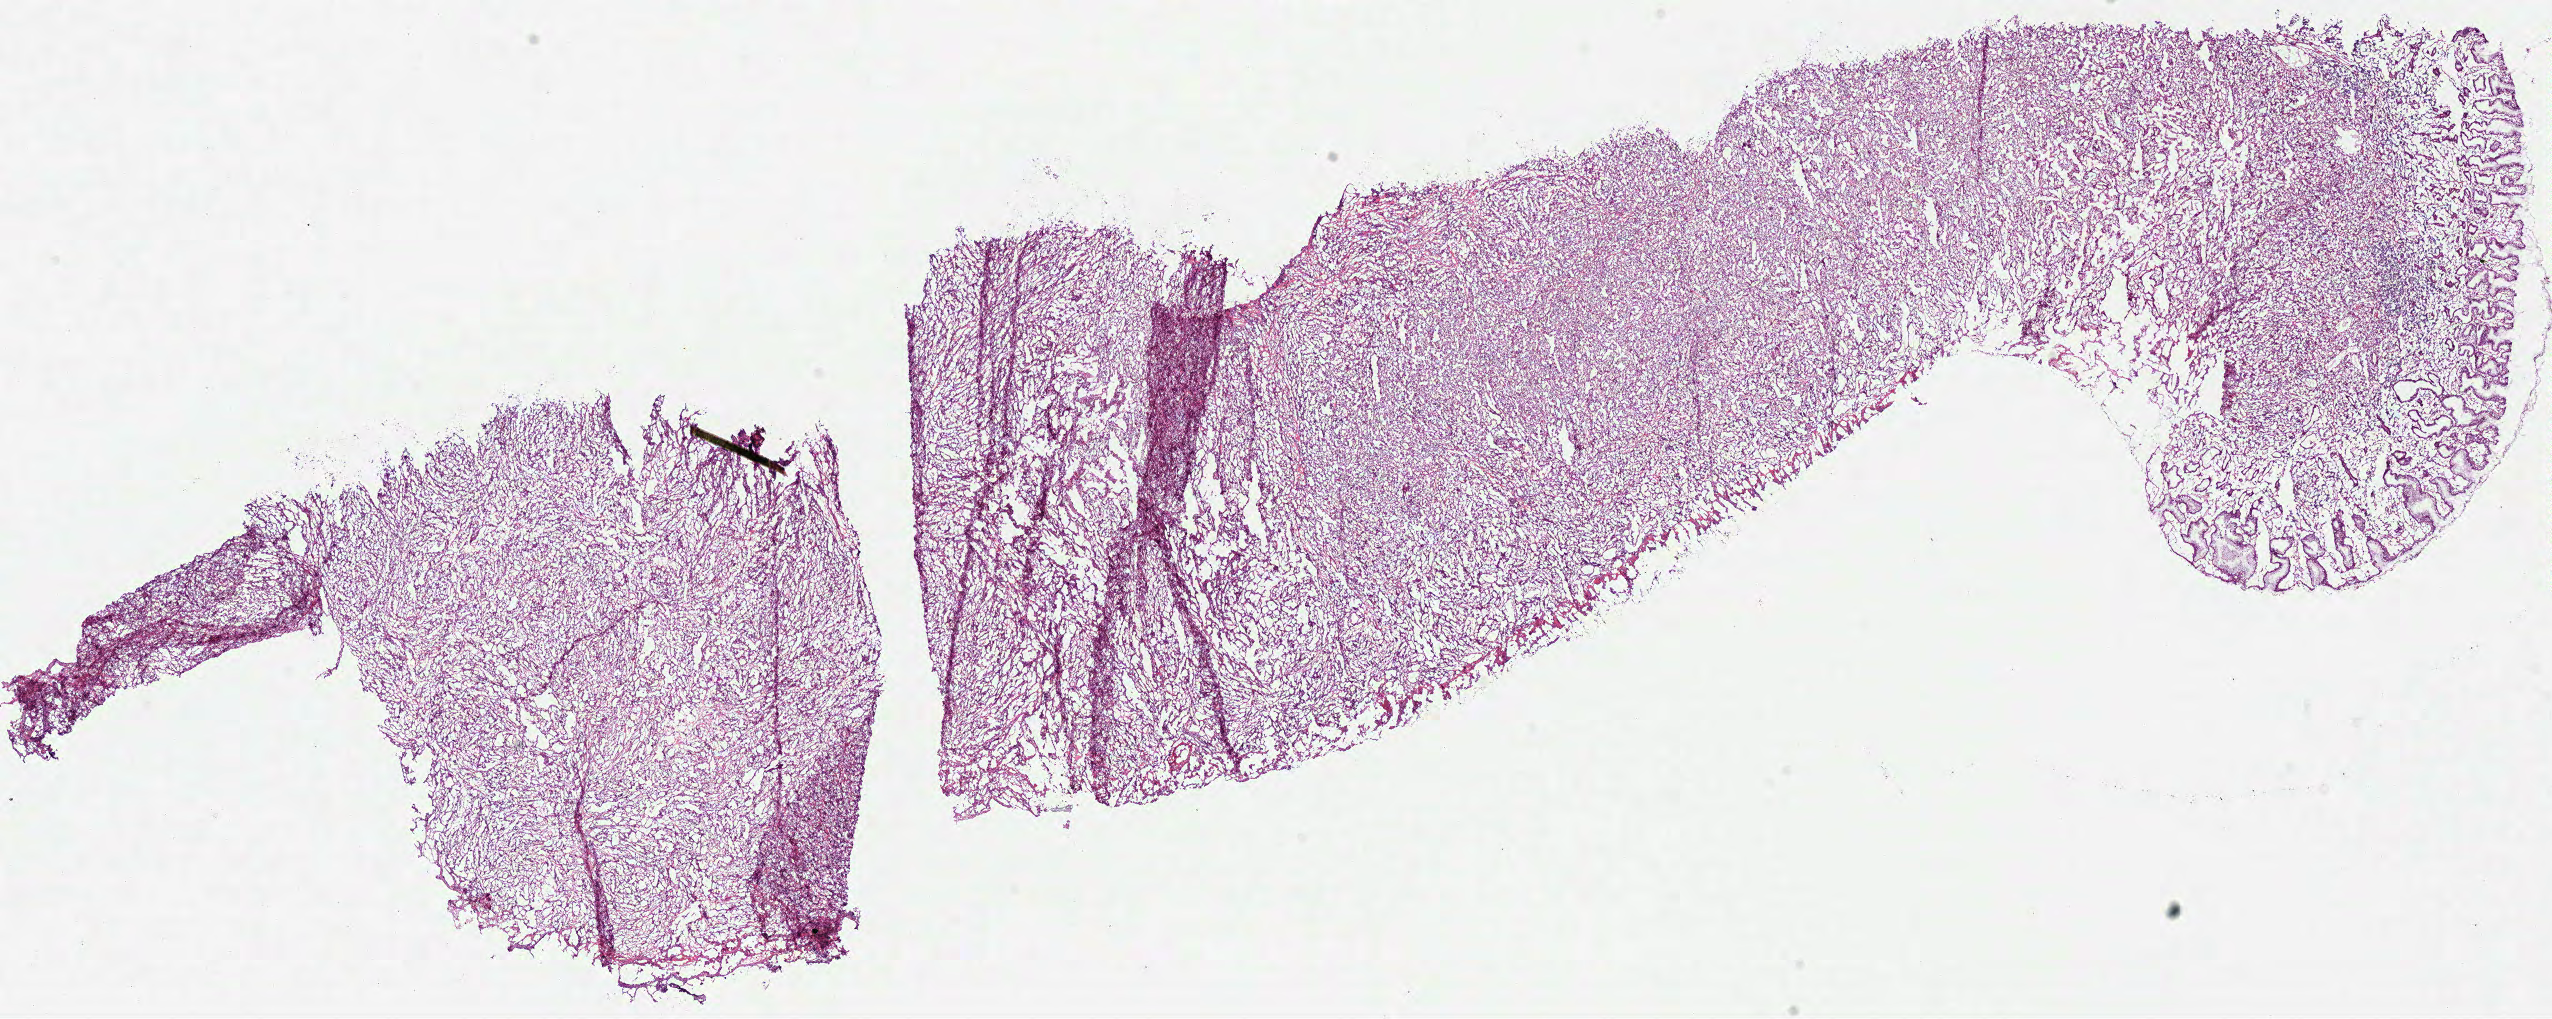
Hematoxylin and eosin (H&E) stained whole-slide image, whole scanned area (about 20.1 x 8.0 mm) shown as a low-resolution overview; frozen section from the top of the tissue portion; stomach, primary tumour sample. Male patient; age at initial diagnosis 65 years. Histologic grade: G3 (poorly differentiated). Pathologist review of this section (percent, as recorded): tumour cells 77%, tumour nuclei 75%, normal cells 8%, stromal cells 10%, necrosis 5%.
• diagnosis: Adenocarcinoma, NOS (body of stomach)
• AJCC pathologic stage: IIIA (7th edition)
• lymph nodes positive (case pathology): 3 of 3 examined